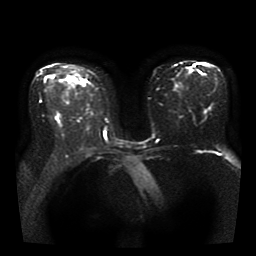
Breast MRI, one axial slice. Slice 21 of 41 in the series (ordered by position). Diffusion-weighted series; image 2 of 4 stored at this slice position (different b-values; order by instance number). 1.5 T. 5 mm slice thickness. 256 × 256 image matrix, field of view 330 × 330 mm. Female patient.
Outlined on this slice (manually delineated by an expert):
- tumour on diffusion-weighted imaging: bounding box [x1, y1, x2, y2] px = [81, 80, 84, 82]